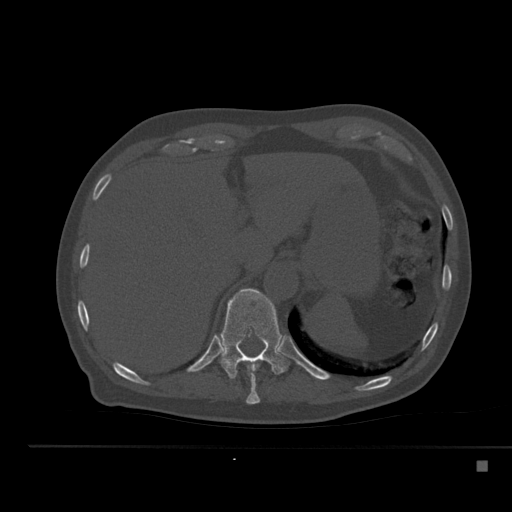
CT including the spine, one axial slice; position 253 of 517 along the scan axis; reconstruction kernel Br40s; 120 kVp; bone window (W 1800 / L 400 HU); 1.5 mm slice thickness; 512 × 512 image matrix, field of view 408 × 408 mm. Male patient, age 70 years. Case-level facts recorded for this patient, not image findings: primary cancer: renal; vertebrae with lytic lesions (as recorded): T4, T6, T10, T12, L3, L4, L5.
Outlined on this slice (semi-automatically segmented with operator editing):
- T10 vertebra: bounding box <246,360,260,405> (left, top, right, bottom; pixels)
- T11 vertebra: <220,288,289,379>